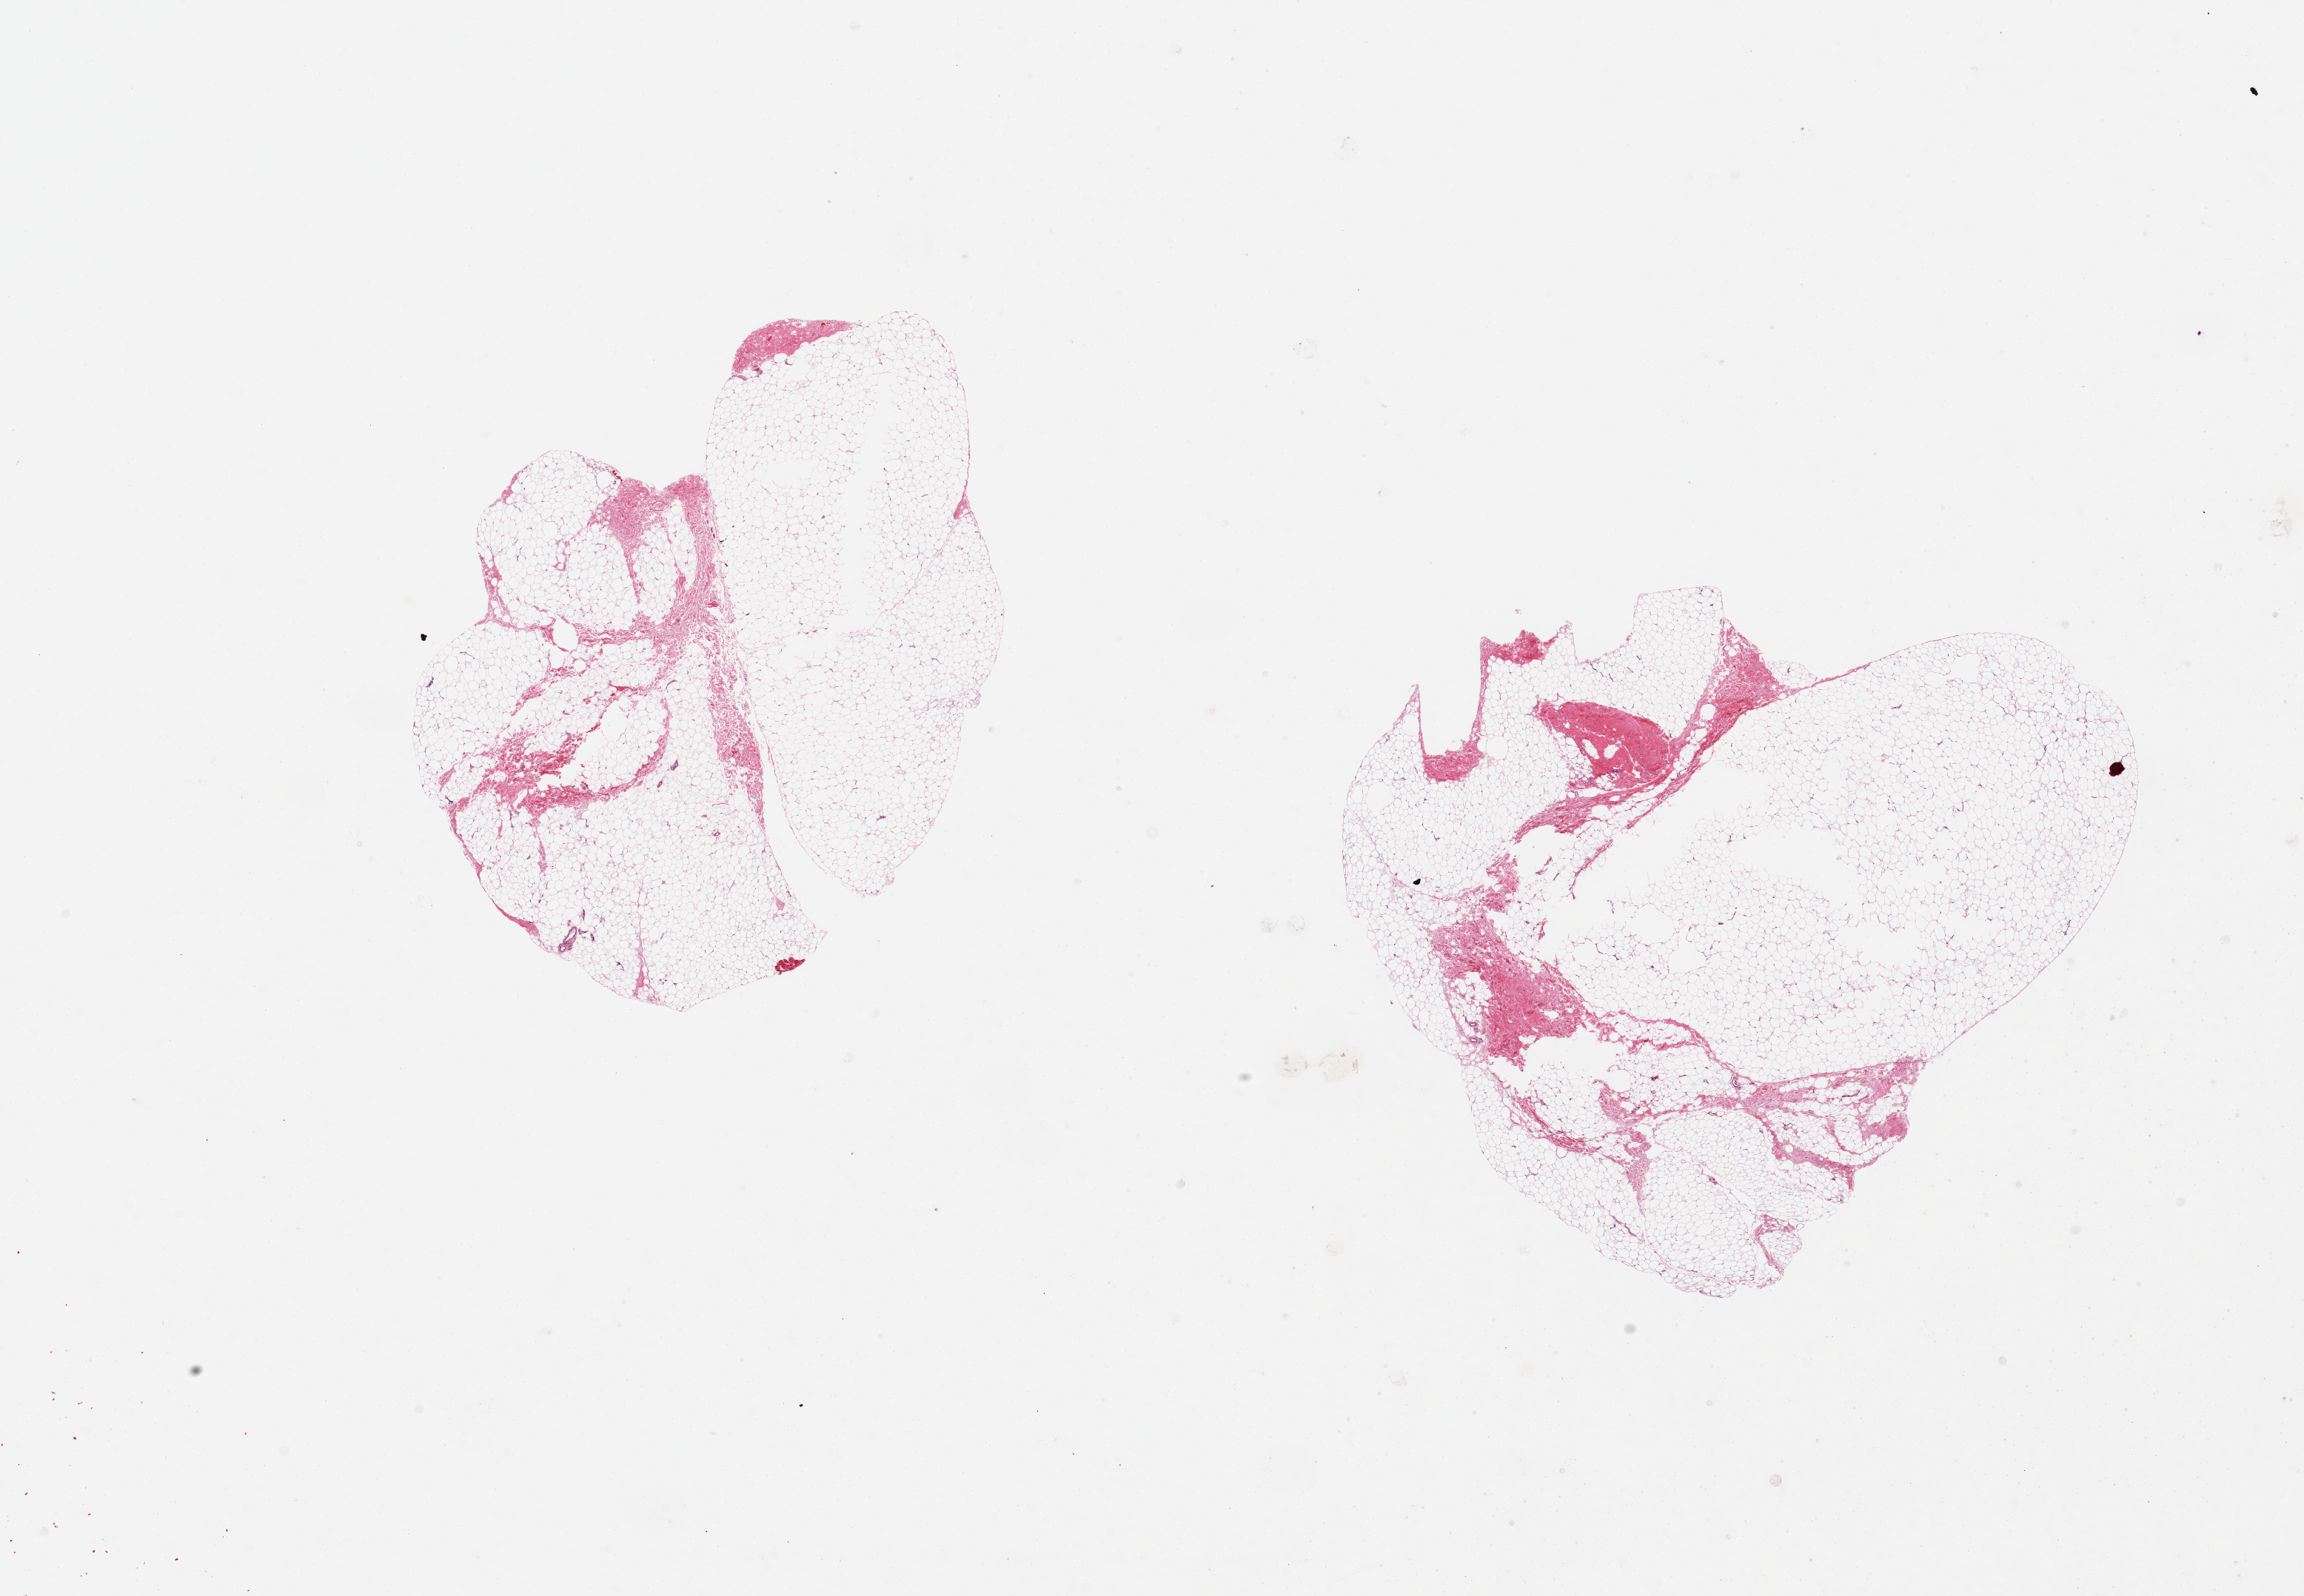
Digitized hematoxylin and eosin (H&E)-stained section — shown as a low-resolution overview of the whole scanned area (about 24.6 x 17.1 mm, from a 20x scan); PAXgene-fixed paraffin-embedded (PFPE) section; section of breast (target tissue); tissue donor sample.
Review note (as recorded): 2 pieces, 6x8 & 7x8mm; no mammary ducts, all adipose.